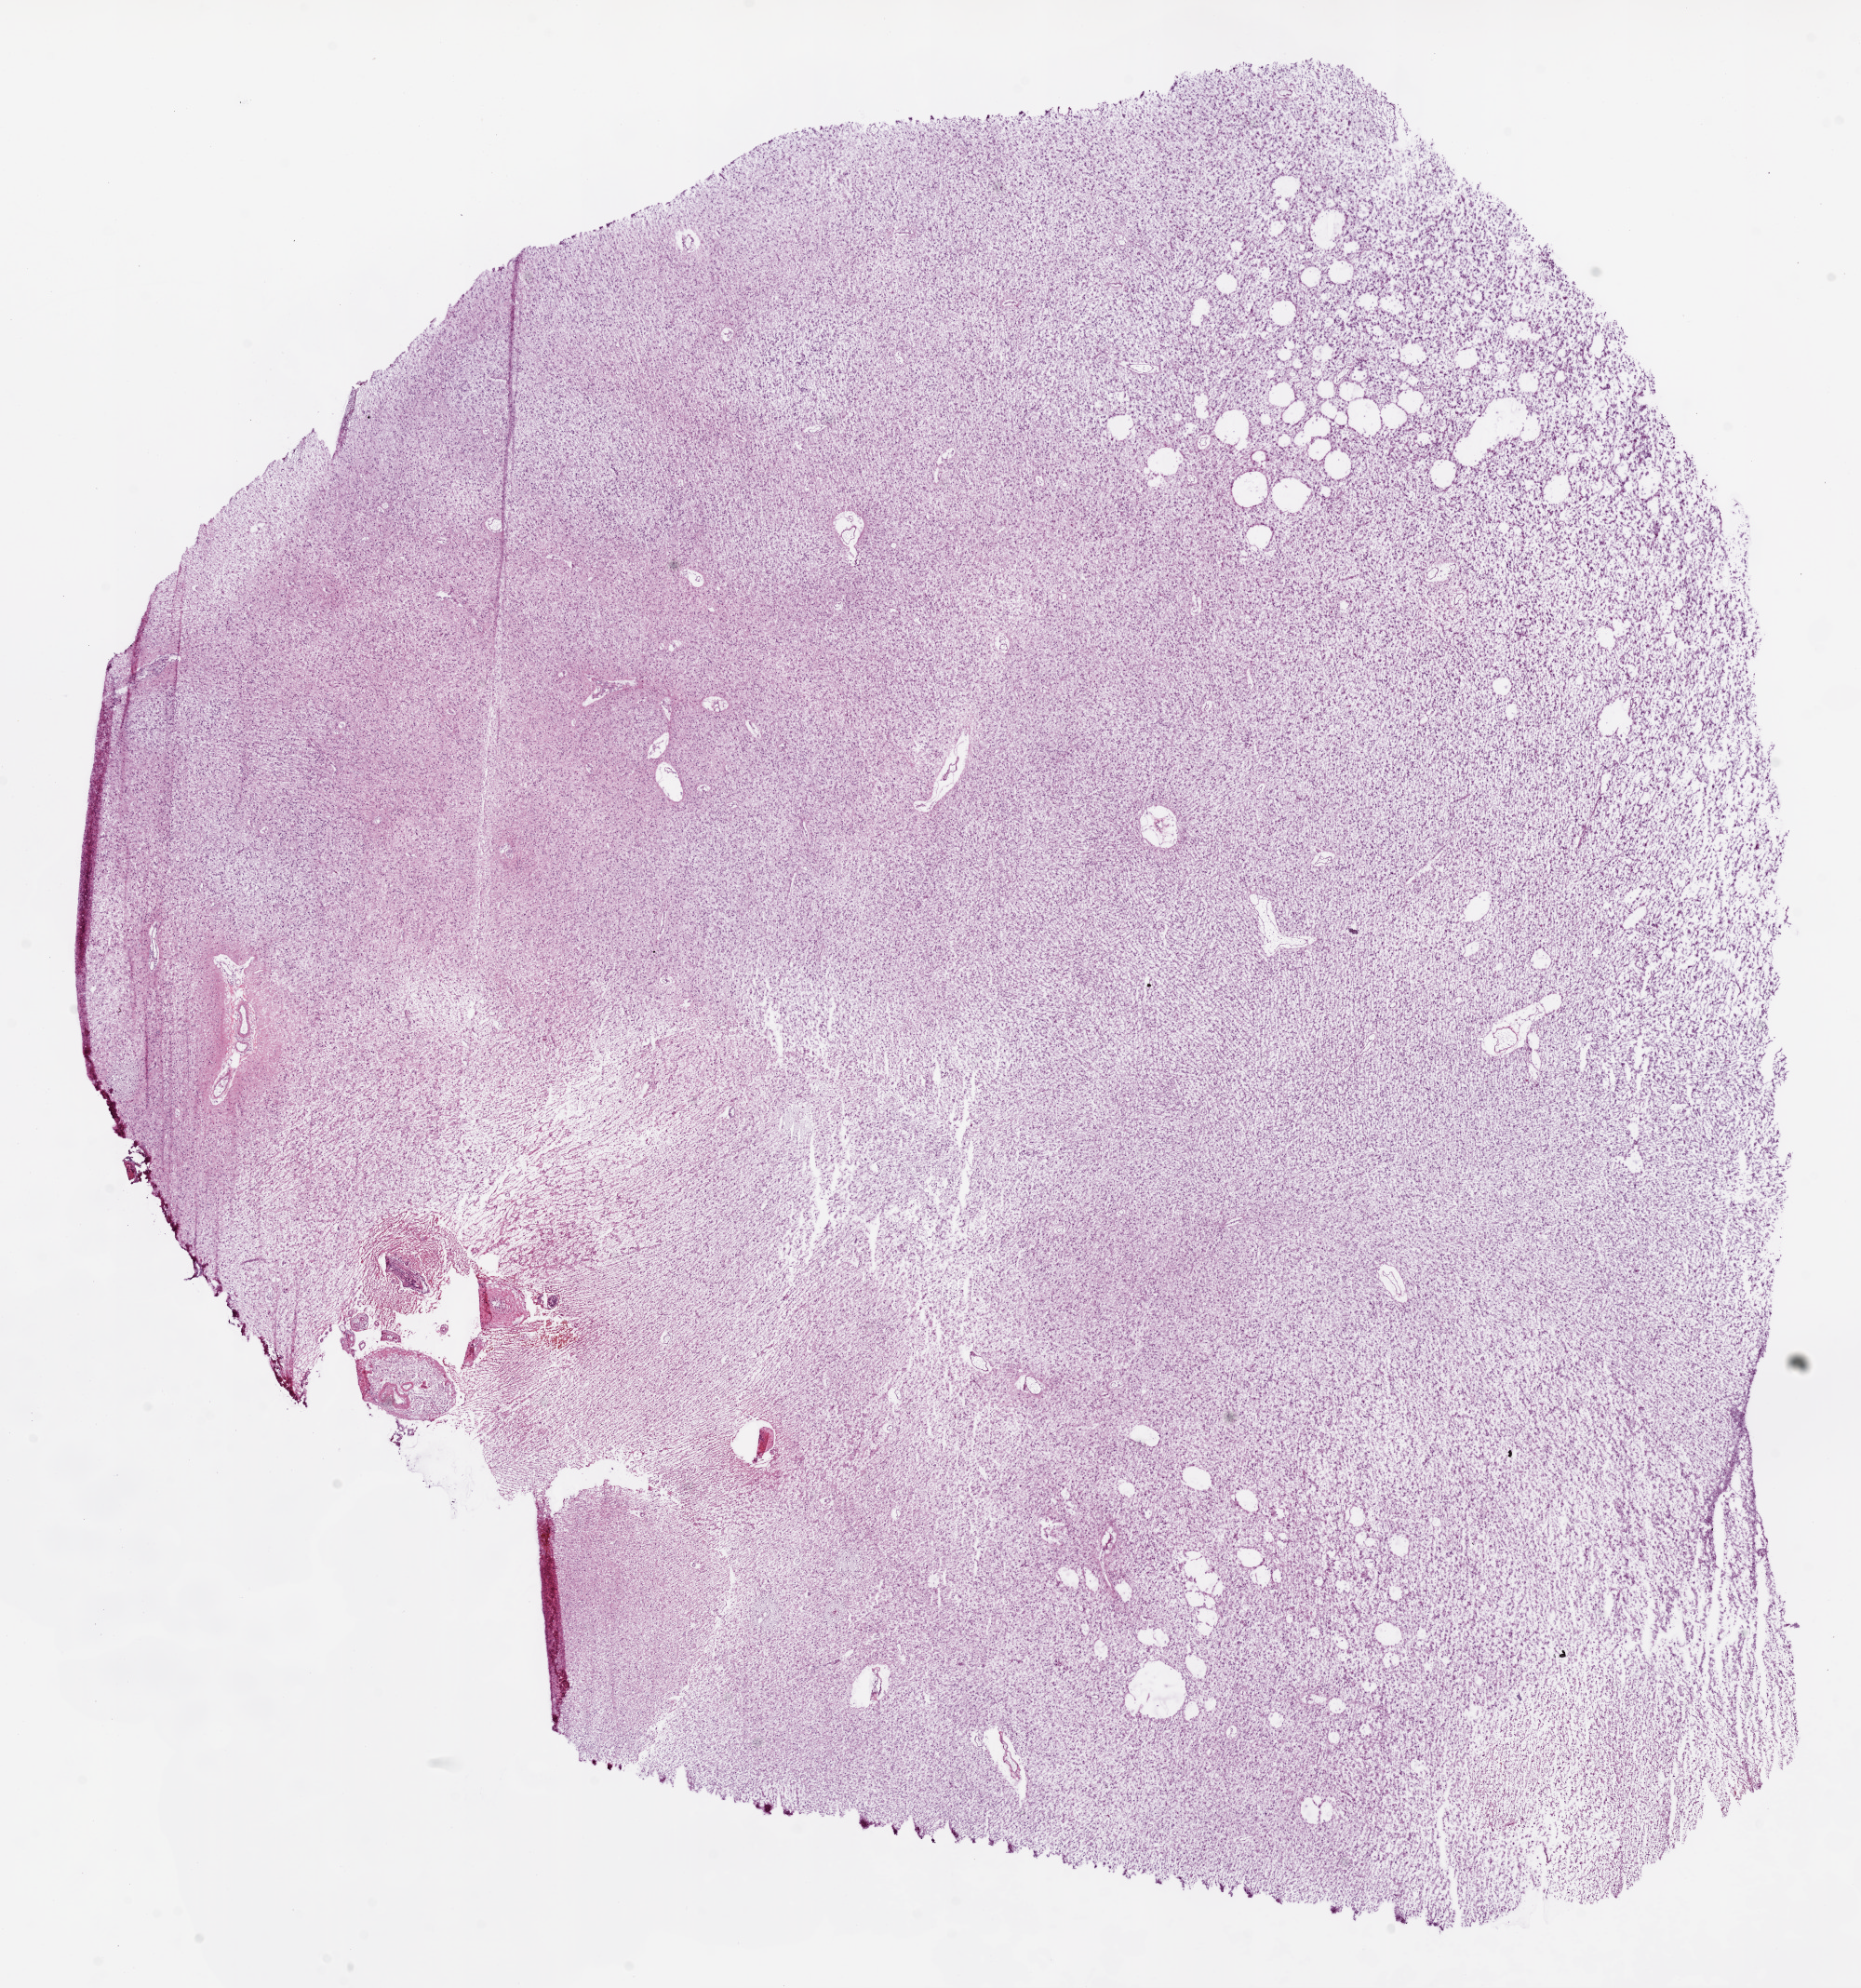
Whole-slide histology image, Hematoxylin and eosin (H&E) stained — low-resolution overview of the scanned area, about 16.0 x 17.1 mm (slide scanned at 20x); frozen section from the top of the tissue portion; brain, primary tumour sample. Male, age 43 years at initial diagnosis. Histologic grade: G2 (moderately differentiated). Pathologist review of this section (percent, as recorded): tumour cells 100%, tumour nuclei 70%, normal cells 0%, stromal cells 0%, necrosis 0%.
- histologic diagnosis: Mixed glioma (cerebrum)